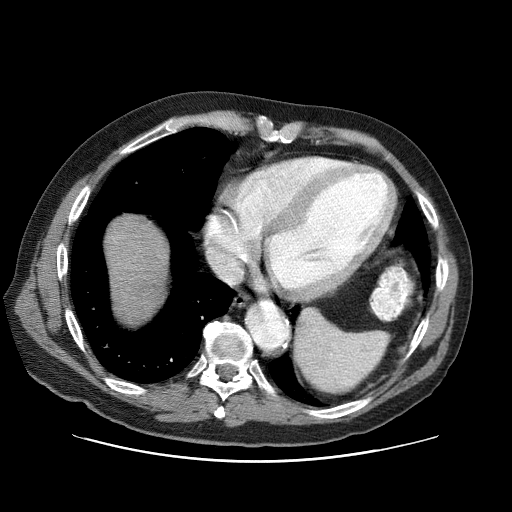
Contrast-enhanced abdominal CT (liver protocol), one axial slice; position 72 of 87 along the scan axis; one of 3 acquisitions stored at this slice position; soft-tissue window (W 400 / L 40 HU); 512 × 512 image matrix, field of view 400 × 400 mm. From the clinical record (not read from this slice): diagnosis: hepatocellular carcinoma (patient treated with transarterial chemoembolisation; whether this scan precedes or follows treatment is not stated here); TNM stage (as recorded): Stage-IIIA; Child-Pugh class: A.
Outlined on this slice (semi-automatic segmentation, software-assisted and operator-edited):
- liver parenchyma outside the tumour (the mass and vessels are separate outlines, so this box may not span the whole liver): bounding box (x1, y1, x2, y2) in pixels: (106, 214, 168, 320)